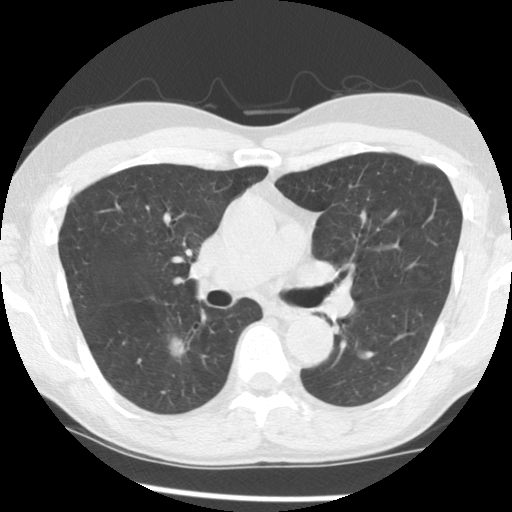
Low-dose screening chest CT, one axial slice; position 83 of 145 along the scan axis; 140 kVp; lung window (W 1500 / L -600 HU); 2.5 mm slice thickness; 512 × 512 image matrix, field of view 320 × 320 mm.
Outlined on this slice (outlined manually by an expert reader):
- lesion 1 (tumor, lower lobe of right lung): bounding box (x1, y1, x2, y2) in pixels: (169, 338, 186, 356)